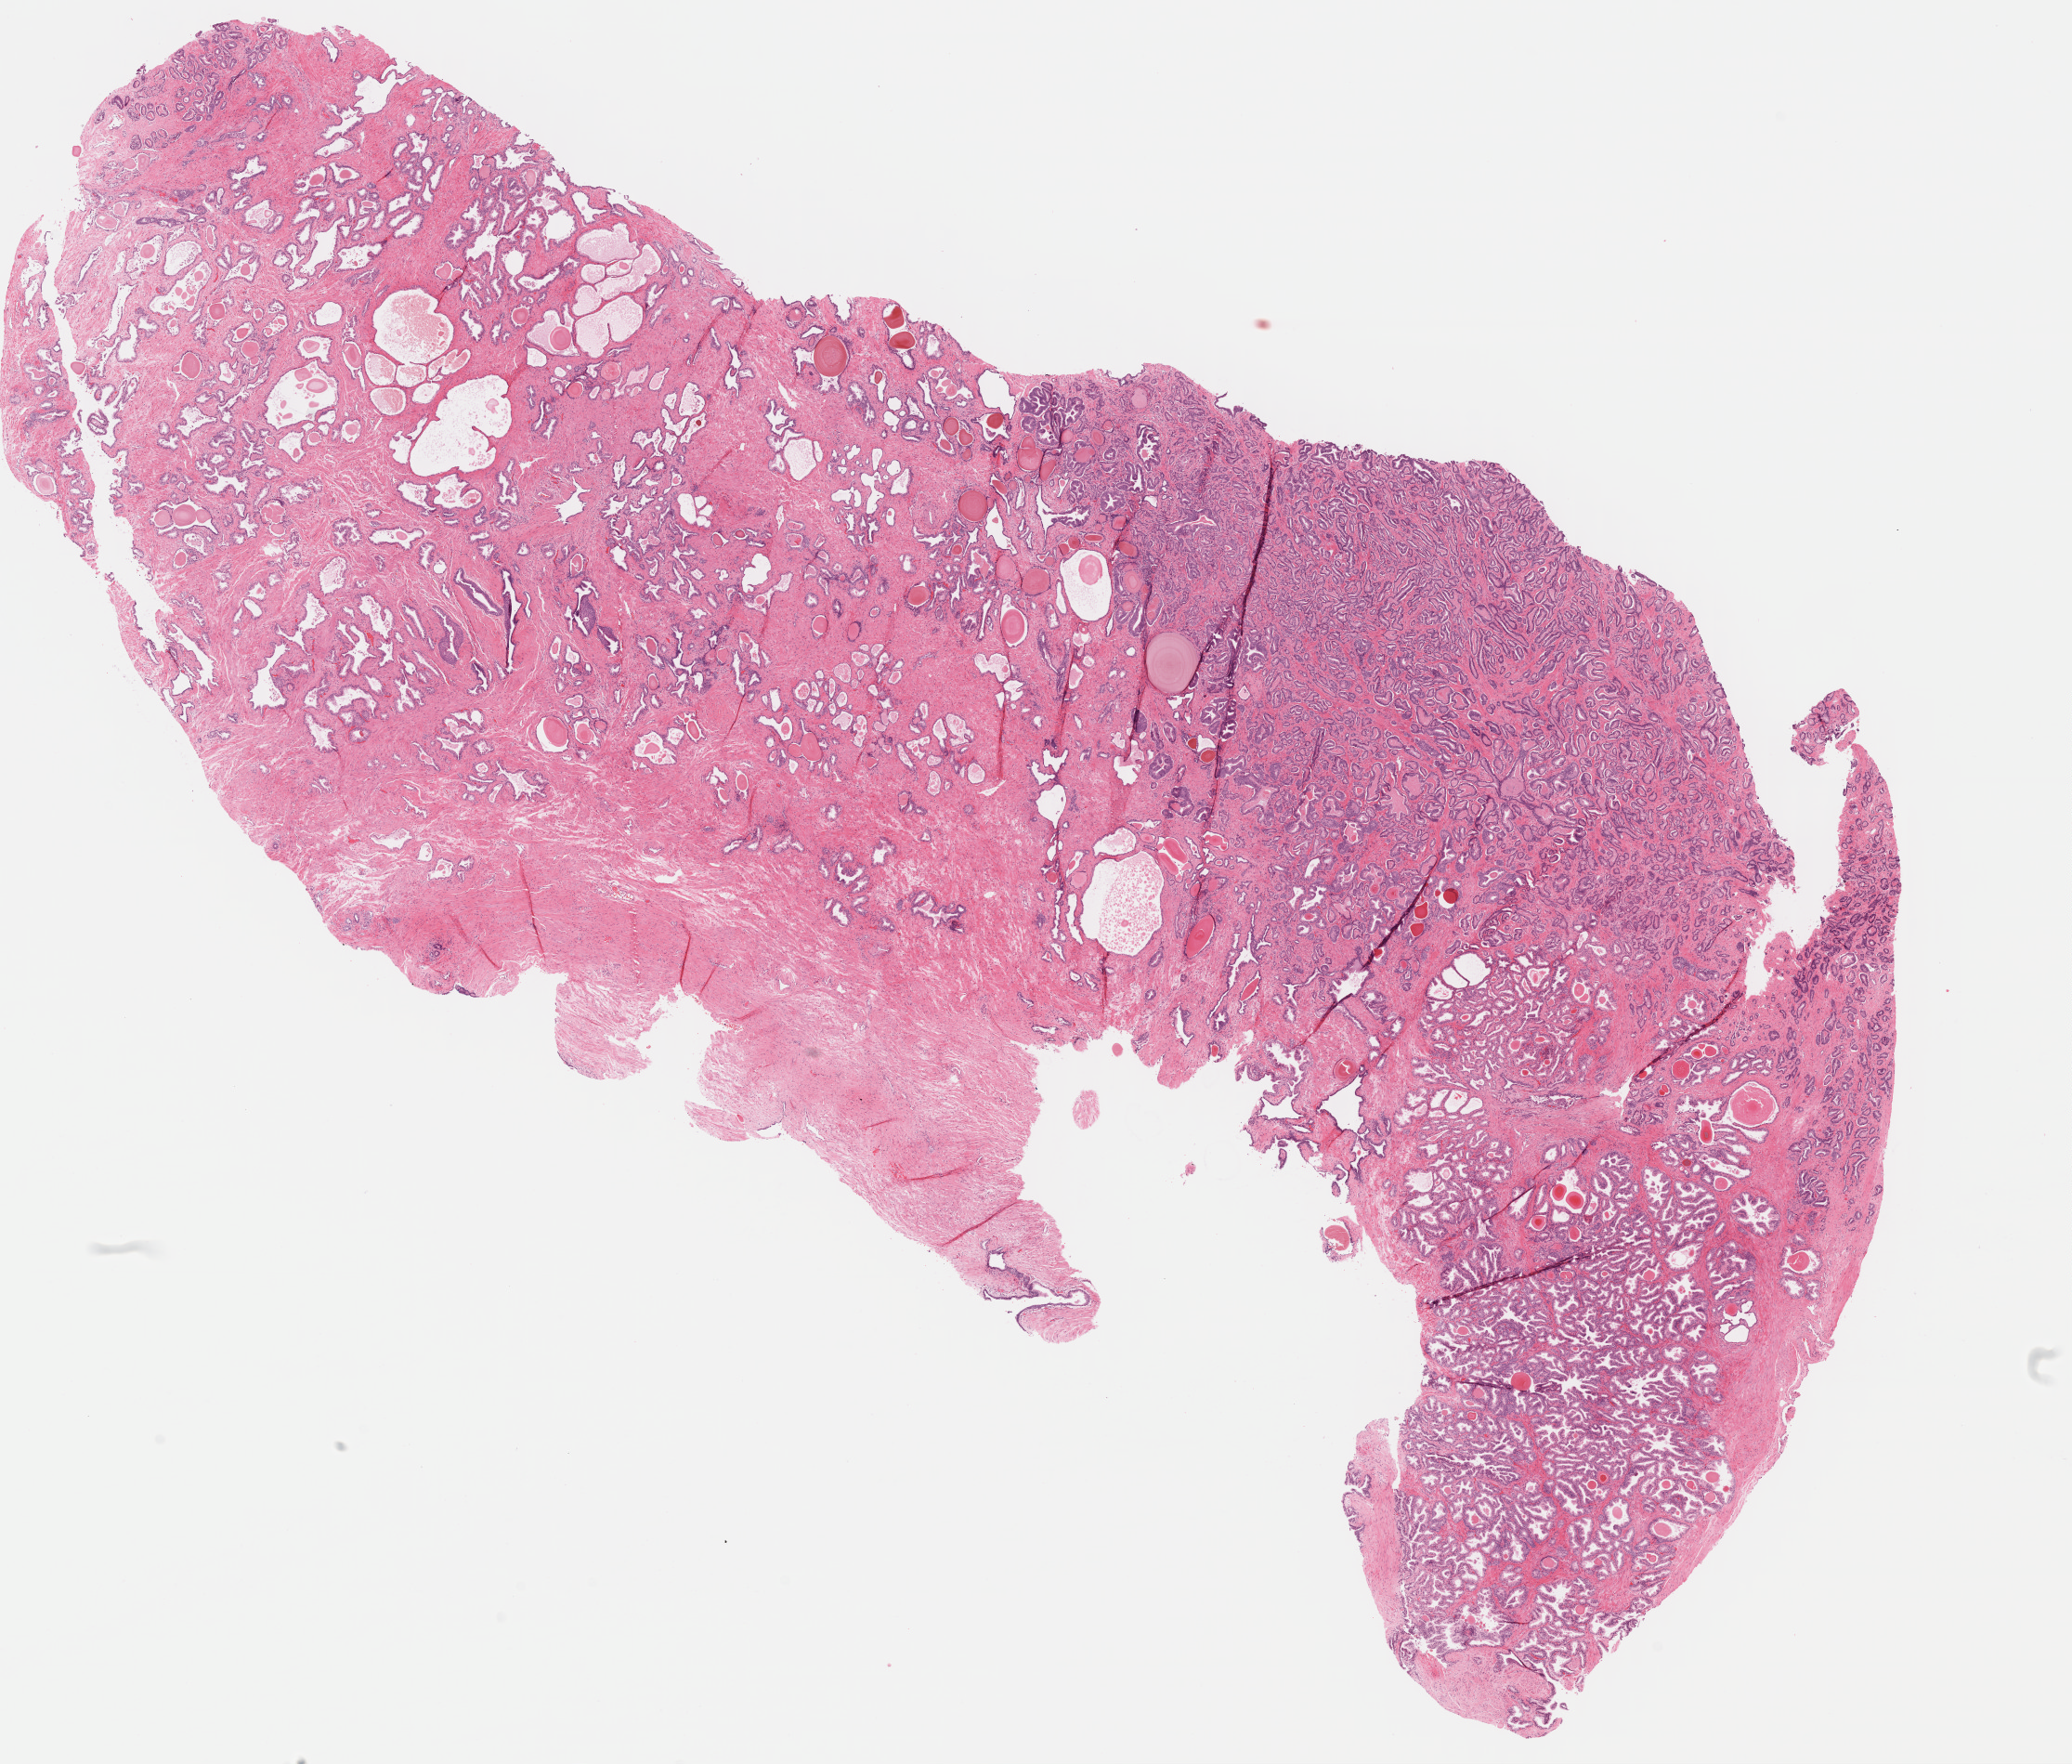
Whole-slide histology image, H&E-stained — low-resolution overview of the scanned area, about 17.5 x 14.9 mm (from a 40x scan). Formalin-fixed paraffin-embedded (FFPE) diagnostic section. Sample: primary tumour, prostate. Male, age 74 years at initial diagnosis. Gleason score: 7 (4+3).
Diagnosis: Adenocarcinoma, NOS. Lymph nodes positive (case pathology): 0 of 2 examined. Laterality: bilateral.